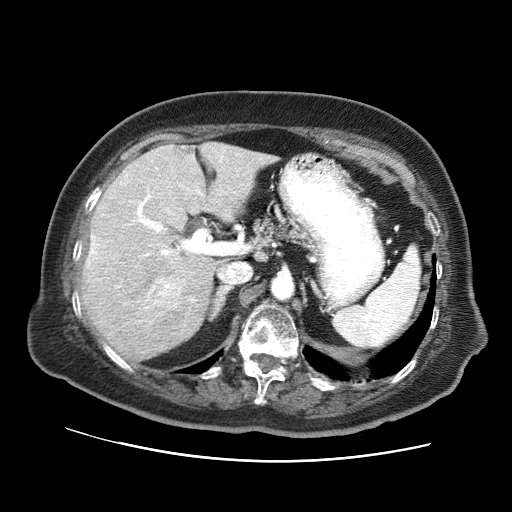
Contrast-enhanced abdominal CT (liver protocol), one axial slice. Position 41 of 73 along the scan axis. 120 kVp. Soft-tissue window (W 400 / L 40 HU). 2.5 mm slice thickness. 512 × 512 image matrix. From the clinical record (not read from this slice): diagnosis: hepatocellular carcinoma (patient treated with transarterial chemoembolisation; whether this scan precedes or follows treatment is not stated here); TNM stage (as recorded): Stage-I; Child-Pugh class: A; tumour differentiation: well differentiated; tumour nodularity: uninodular.
Annotated regions visible in this slice (semi-automatic segmentation, software-assisted and operator-edited):
- liver parenchyma outside the tumour (the mass and vessels are separate outlines, so this box may not span the whole liver): box from (x=82, y=142) to (x=277, y=360) px
- mass: (x=145, y=277)–(x=184, y=312)
- liver vessels: (x=88, y=156)–(x=223, y=302)